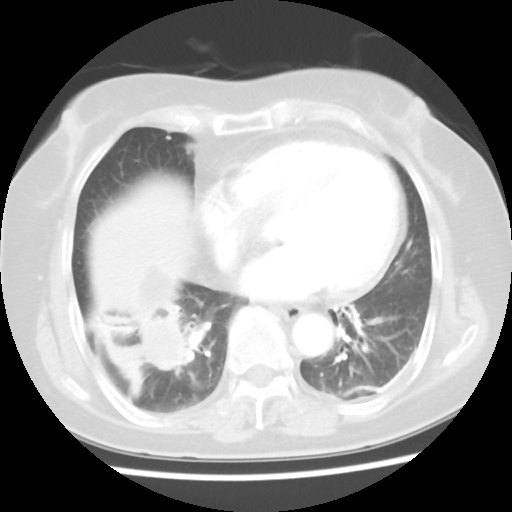
Chest CT, one axial slice; reconstruction kernel STANDARD; 120 kVp; lung window (W 1500 / L -600 HU); 512 × 512 image matrix. Female patient, age 65 years. From the clinical record (not read from this slice): clinical TNM (as recorded): T2 N3 M0.
Structures marked on this image (bounding box drawn by a radiologist):
- lung tumour (recorded histology: adenocarcinoma): bounding box <122,306,202,381> (left, top, right, bottom; pixels)